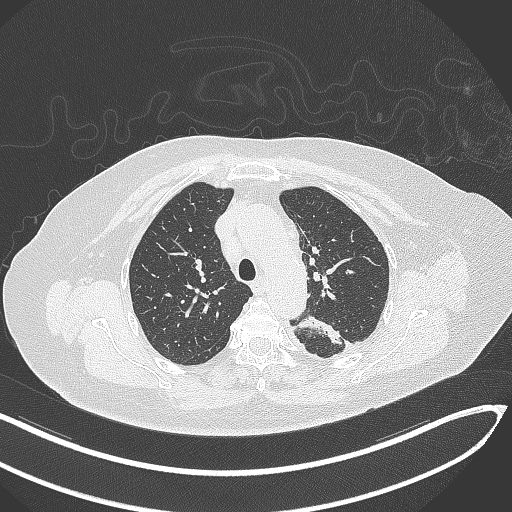
Chest CT, one axial slice; position 230 of 270 along the scan axis; reconstruction kernel B70f; 120 kVp; lung window (W 1500 / L -600 HU); 1 mm slice thickness; 512 × 512 image matrix, field of view 400 × 400 mm. Patient: female, 76 years. Case-level facts recorded for this patient, not image findings: clinical TNM (as recorded): T1c N0 M0.
Structures marked on this image (rectangle marked by the reading radiologist):
- lung tumour (recorded histology: adenocarcinoma): bounding box (x1, y1, x2, y2) in pixels: (293, 312, 349, 349)